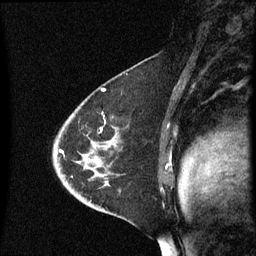
Breast MRI (dynamic contrast-enhanced), one sagittal slice; slice 40 of 60 in the series (ordered by position); dynamic contrast-enhanced series, image 2 of 3 at this slice position (ordered by acquisition); 1.5 T; TE 4.2 ms, TR 8.4 ms; 256 × 256 image matrix, field of view 200 × 200 mm. Patient: female, 46 years. Case-level facts recorded for this patient, not image findings: setting: breast cancer imaged before/during neoadjuvant chemotherapy; receptor status: HER2-positive.
Outlined on this slice (semi-automatic segmentation, software-assisted and operator-edited):
- analysis volume of interest (the breast-tissue region the enhancement analysis was run in; not a lesion): bounding box (x1, y1, x2, y2) in pixels: (53, 98, 167, 187)
- tumour enhancement mask (voxels above the 70 % enhancement threshold inside the analysis volume of interest): (59, 150, 87, 161)